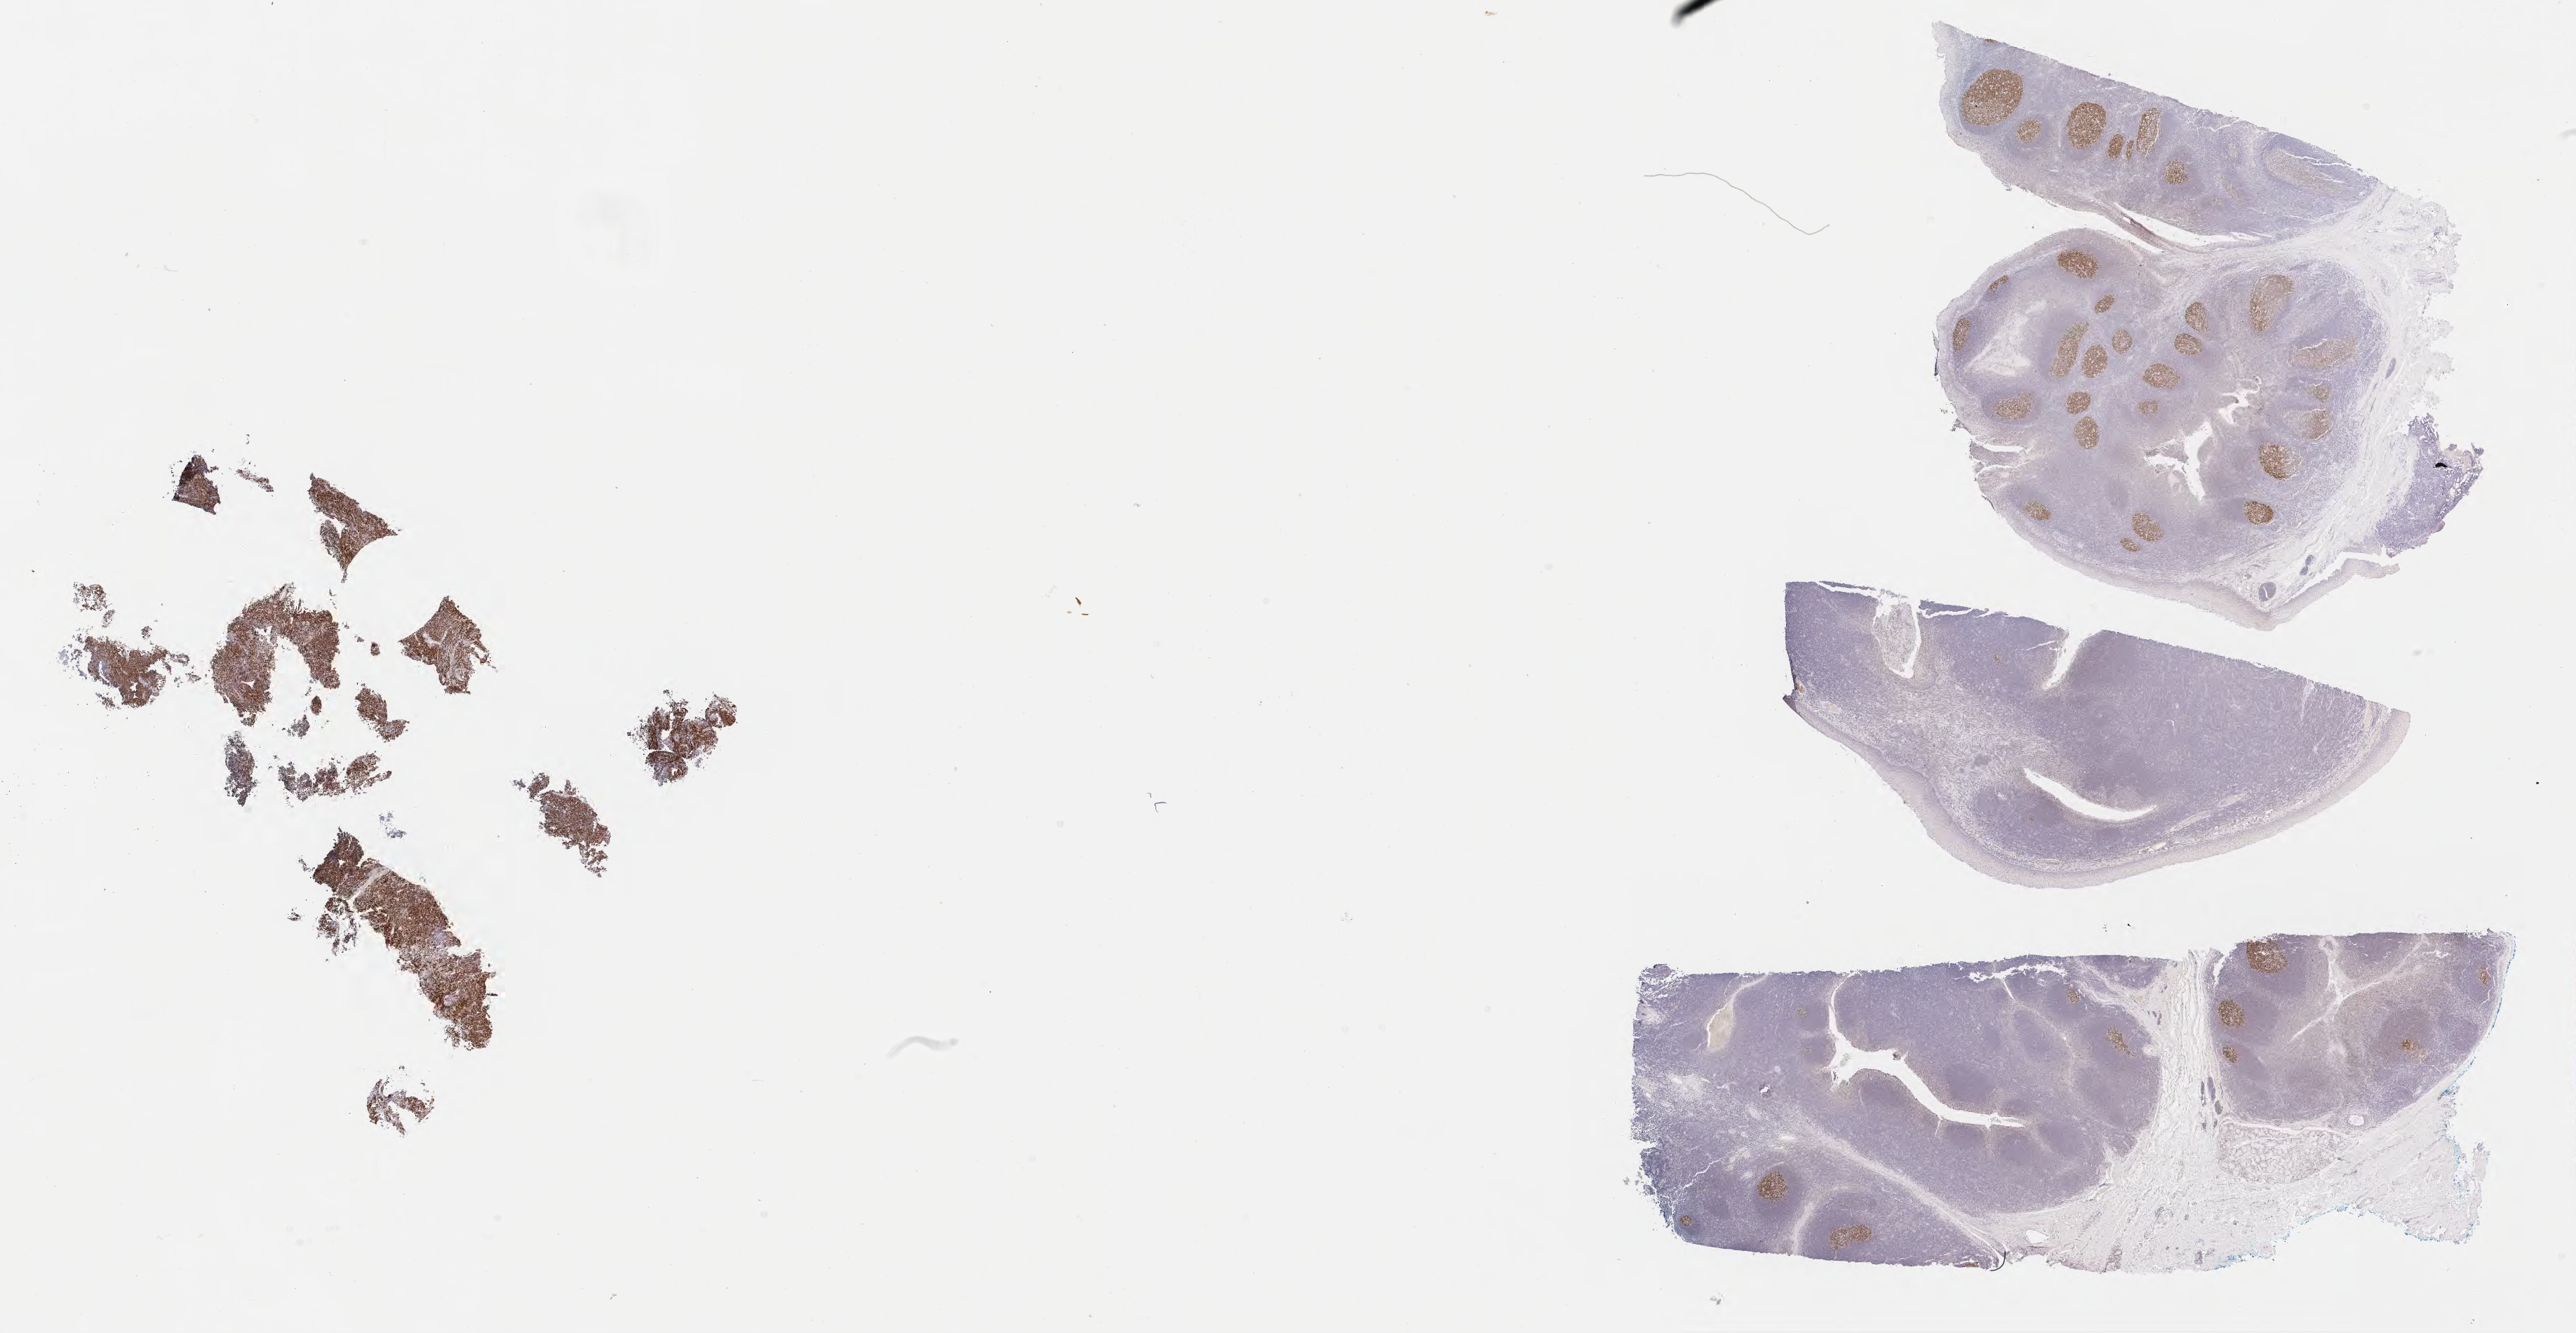
Whole-slide image, immunohistochemical stain for BCL6 — shown as a low-resolution overview of the whole scanned area (about 29.7 x 15.4 mm); tumor tissue; anatomic site: kidney. Female, age 8 years at initial diagnosis.
Histologic diagnosis: Burkitt lymphoma, NOS.